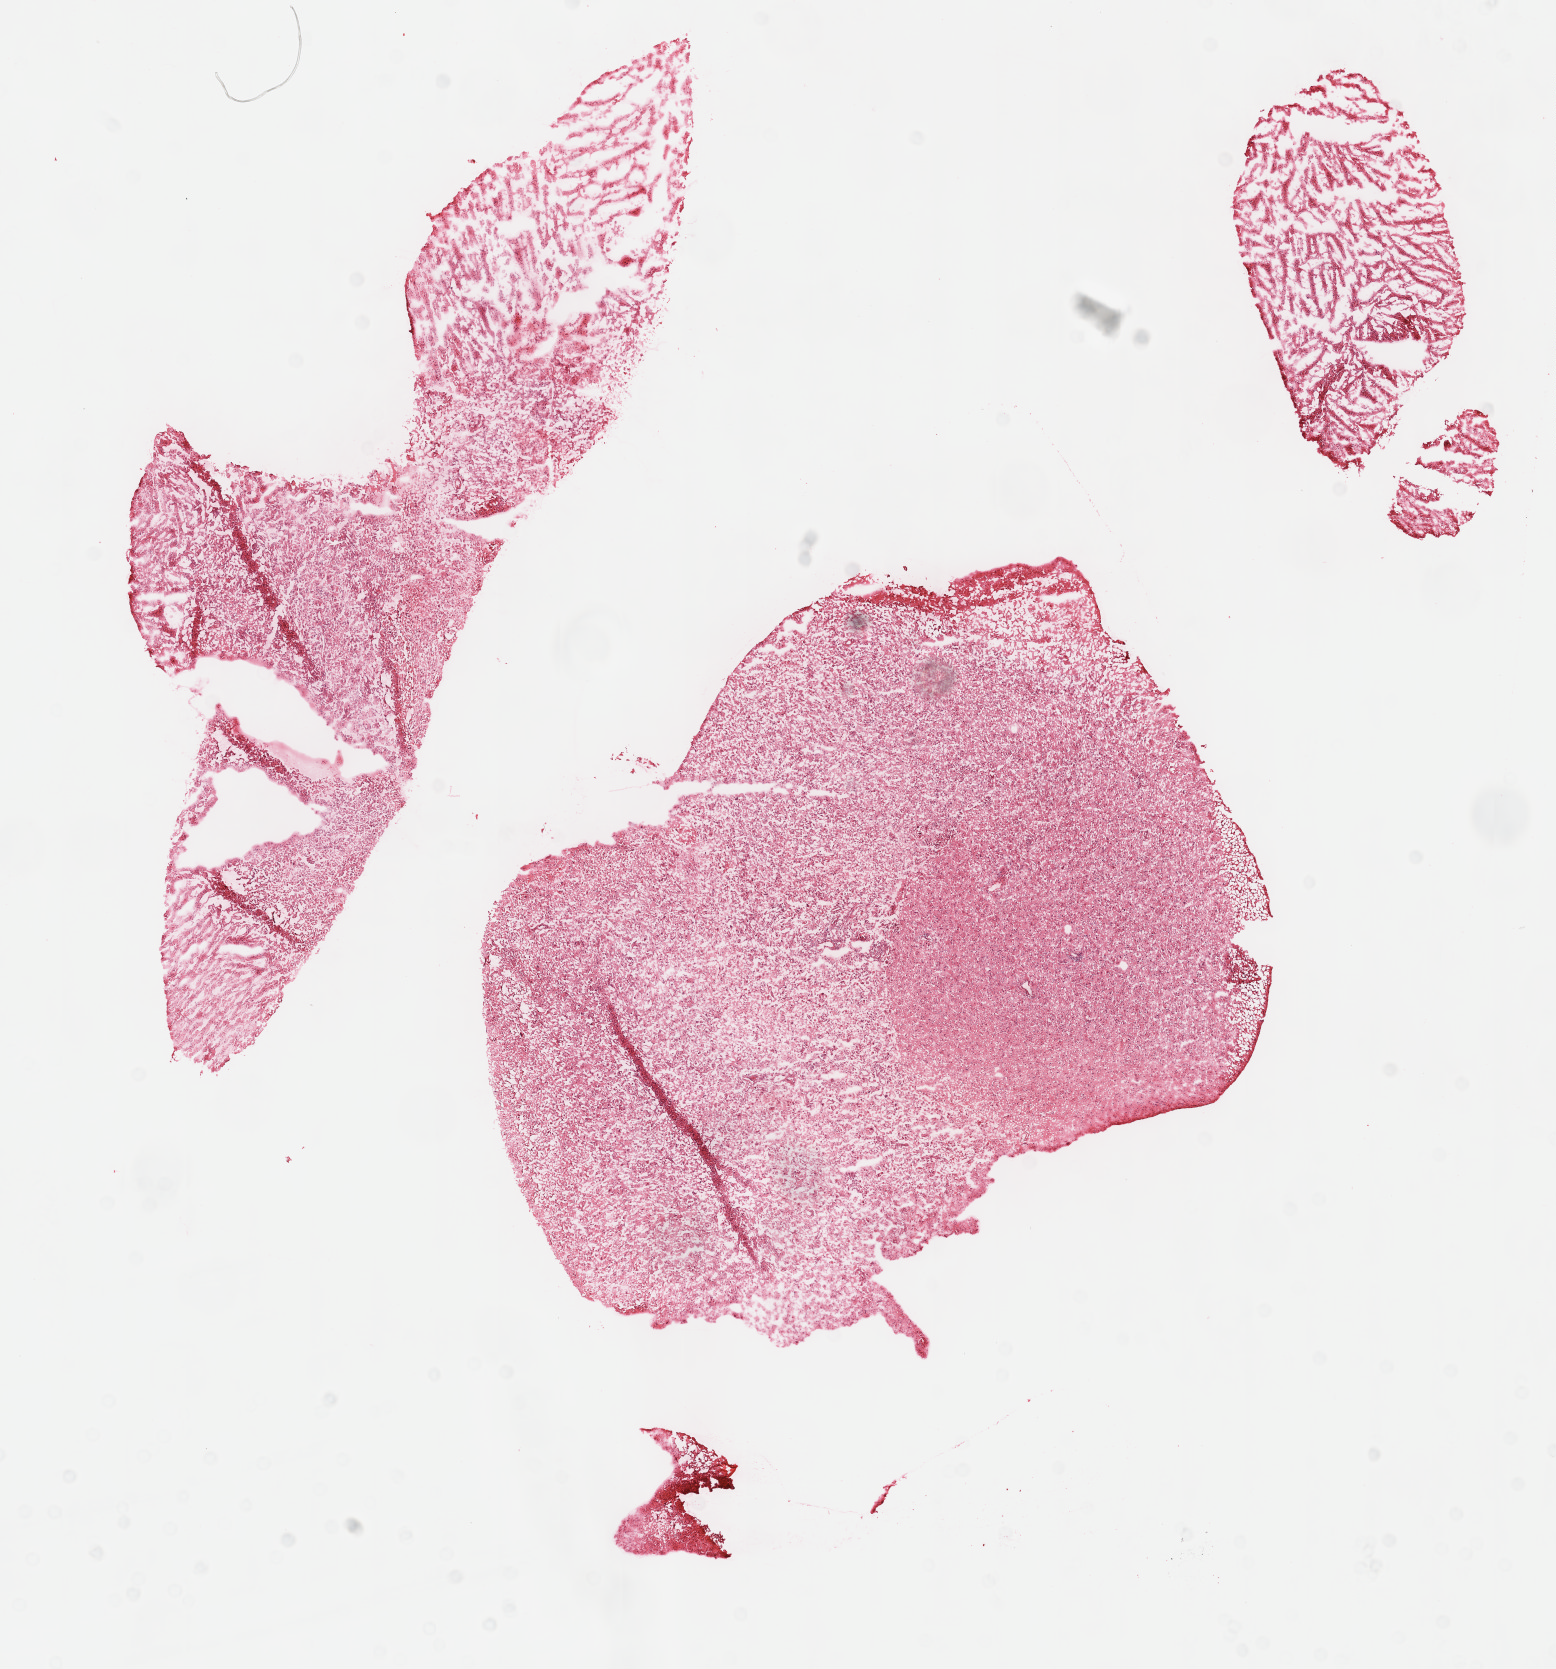
H&E whole-slide image — a low-resolution overview of the entire scanned area, about 12.6 x 13.5 mm (from a 40x scan); frozen section from the top of the tissue portion; primary tumour sample from the brain. Male patient; age at initial diagnosis 46 years. Composition of this section per pathologist review: tumour cells 100%, tumour nuclei 100%, normal cells 0%, stromal cells 0%, necrosis 0%. Inflammatory infiltration, as recorded: lymphocyte infiltration 0%.
Histologic diagnosis: Glioblastoma.